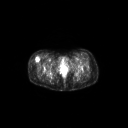
FDG PET of an extremity soft-tissue mass (from a PET/CT study), one axial slice; slice 53 of 267 in the series (ordered by position); 128 × 128 image matrix, field of view 700 × 700 mm. Patient: female, 34 years. Case-level facts recorded for this patient, not image findings: histological type: synovial sarcoma; grade: intermediate; site of the primary tumour: right thigh.
Outlined on this slice (expert contour drawn on MRI and transferred to this co-registered scan by the dataset authors):
- gross tumour volume including surrounding oedema: box from (x=34, y=56) to (x=39, y=62) px
- gross tumour volume (mass): (x=34, y=56)–(x=39, y=62)